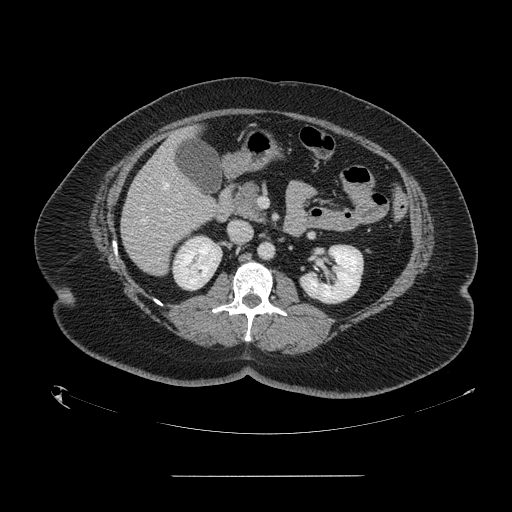
Contrast-enhanced abdominal CT, one axial slice; slice 66 of 164 in the series (ordered by position); 120 kVp; soft-tissue window (W 400 / L 40 HU); 2.5 mm slice thickness; 512 × 512 image matrix, field of view 495 × 495 mm. Female patient, age 52 years. Case-level facts recorded for this patient, not image findings: diagnosis: colorectal cancer liver metastases, imaged before liver resection; multiple liver metastases: yes; largest metastasis: 3.5 cm; chemotherapy before resection: no.
Annotated regions visible in this slice (expert manual segmentation):
- hepatic veins: bounding box [x1, y1, x2, y2] px = [142, 183, 172, 222]
- liver: [122, 130, 218, 275]
- planned liver remnant (the part of the liver to remain after resection): [187, 130, 195, 135]